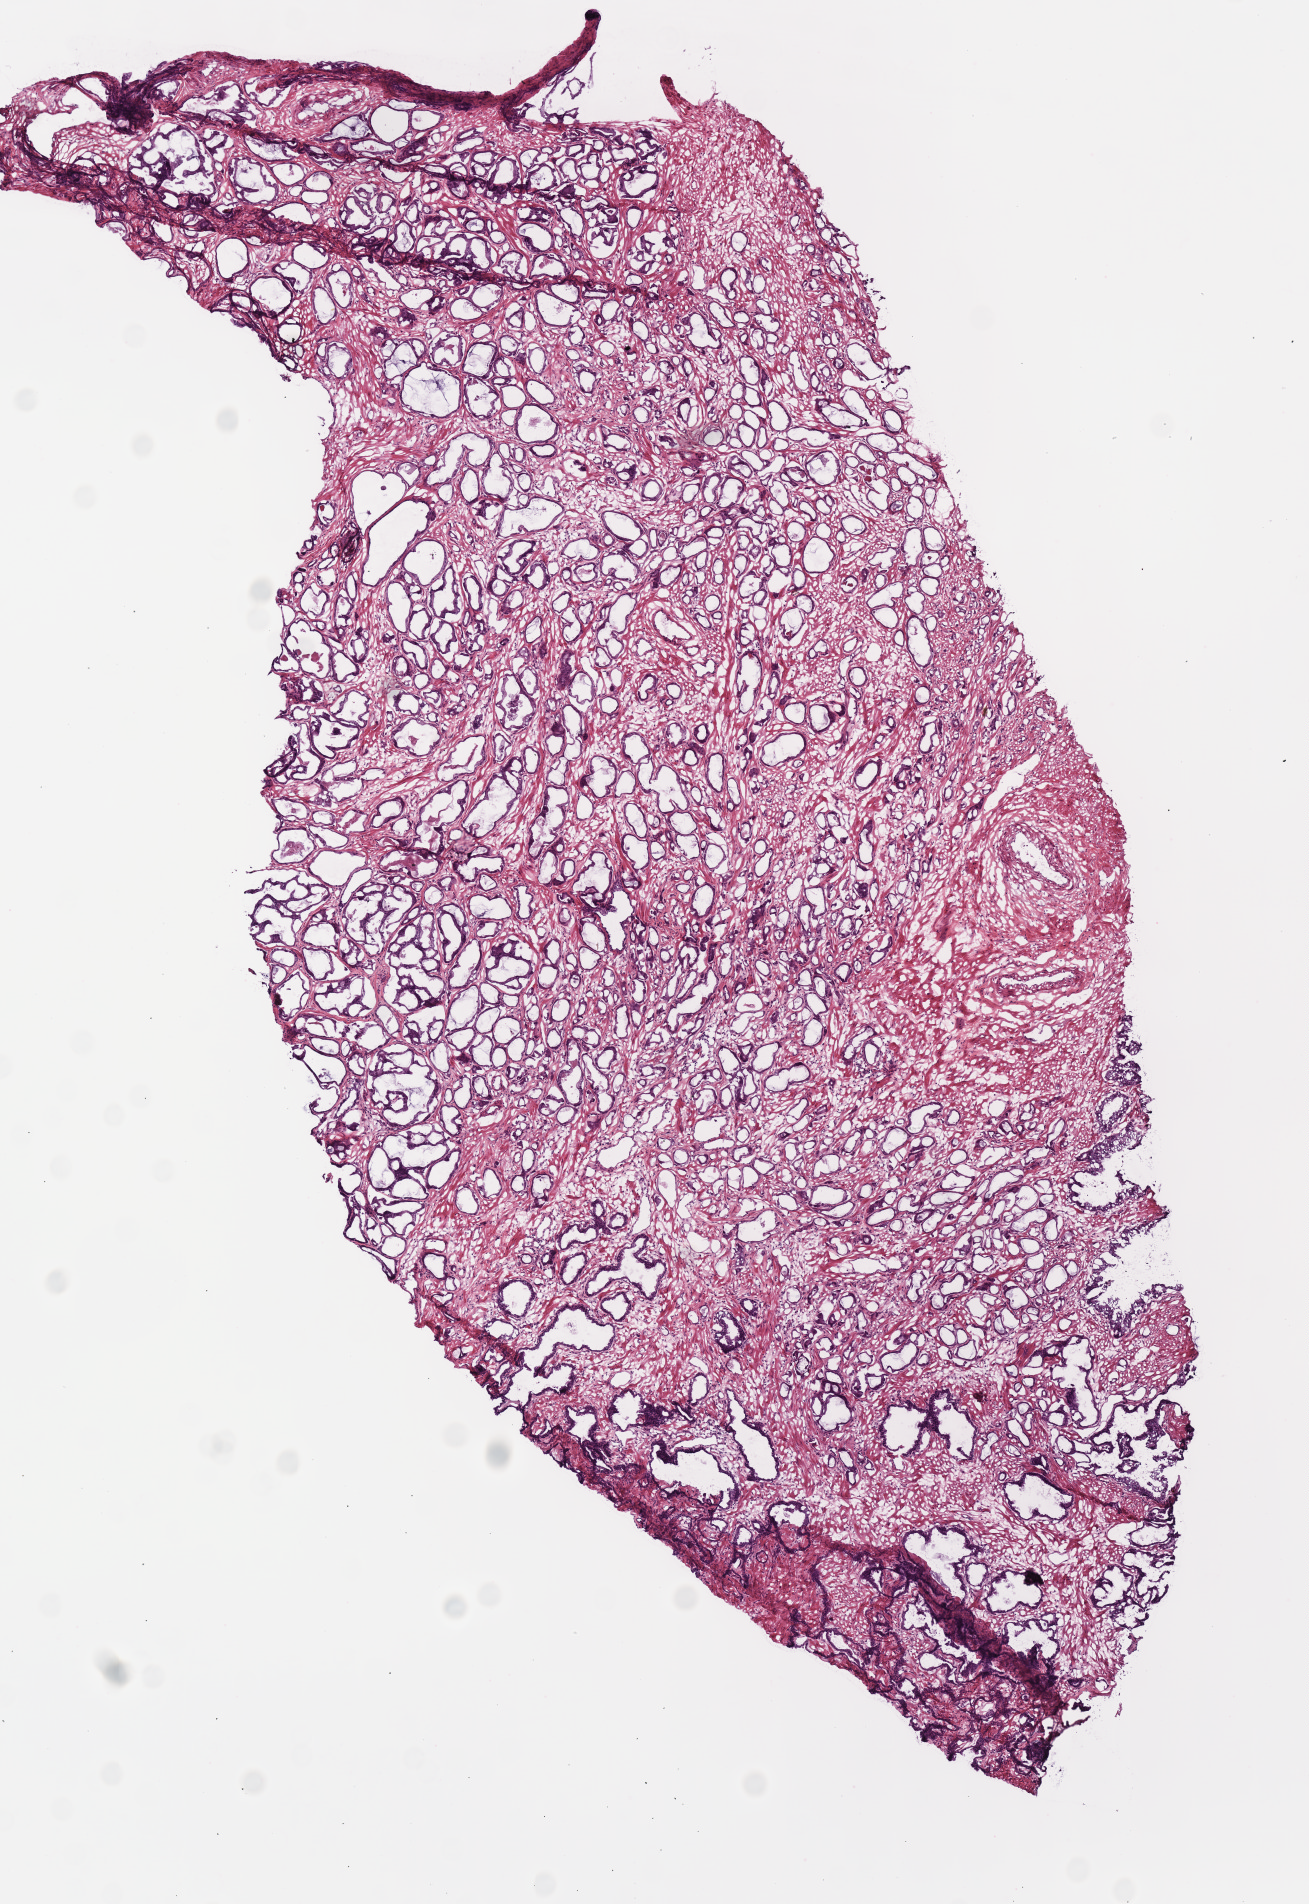
H&E whole-slide image — shown as a low-resolution overview of the whole scanned area (about 5.2 x 7.5 mm); frozen section from the top of the tissue portion; prostate, primary tumour sample. Male patient; age at initial diagnosis 49 years. Gleason score: 7 (3+4). Composition of this section per pathologist review: tumour cells 70%, tumour nuclei 70%, normal cells 20%, stromal cells 10%, necrosis 0%.
- lymph nodes positive (case pathology): 0 of 9 examined
- pathologic diagnosis: Acinar cell carcinoma (prostate gland)